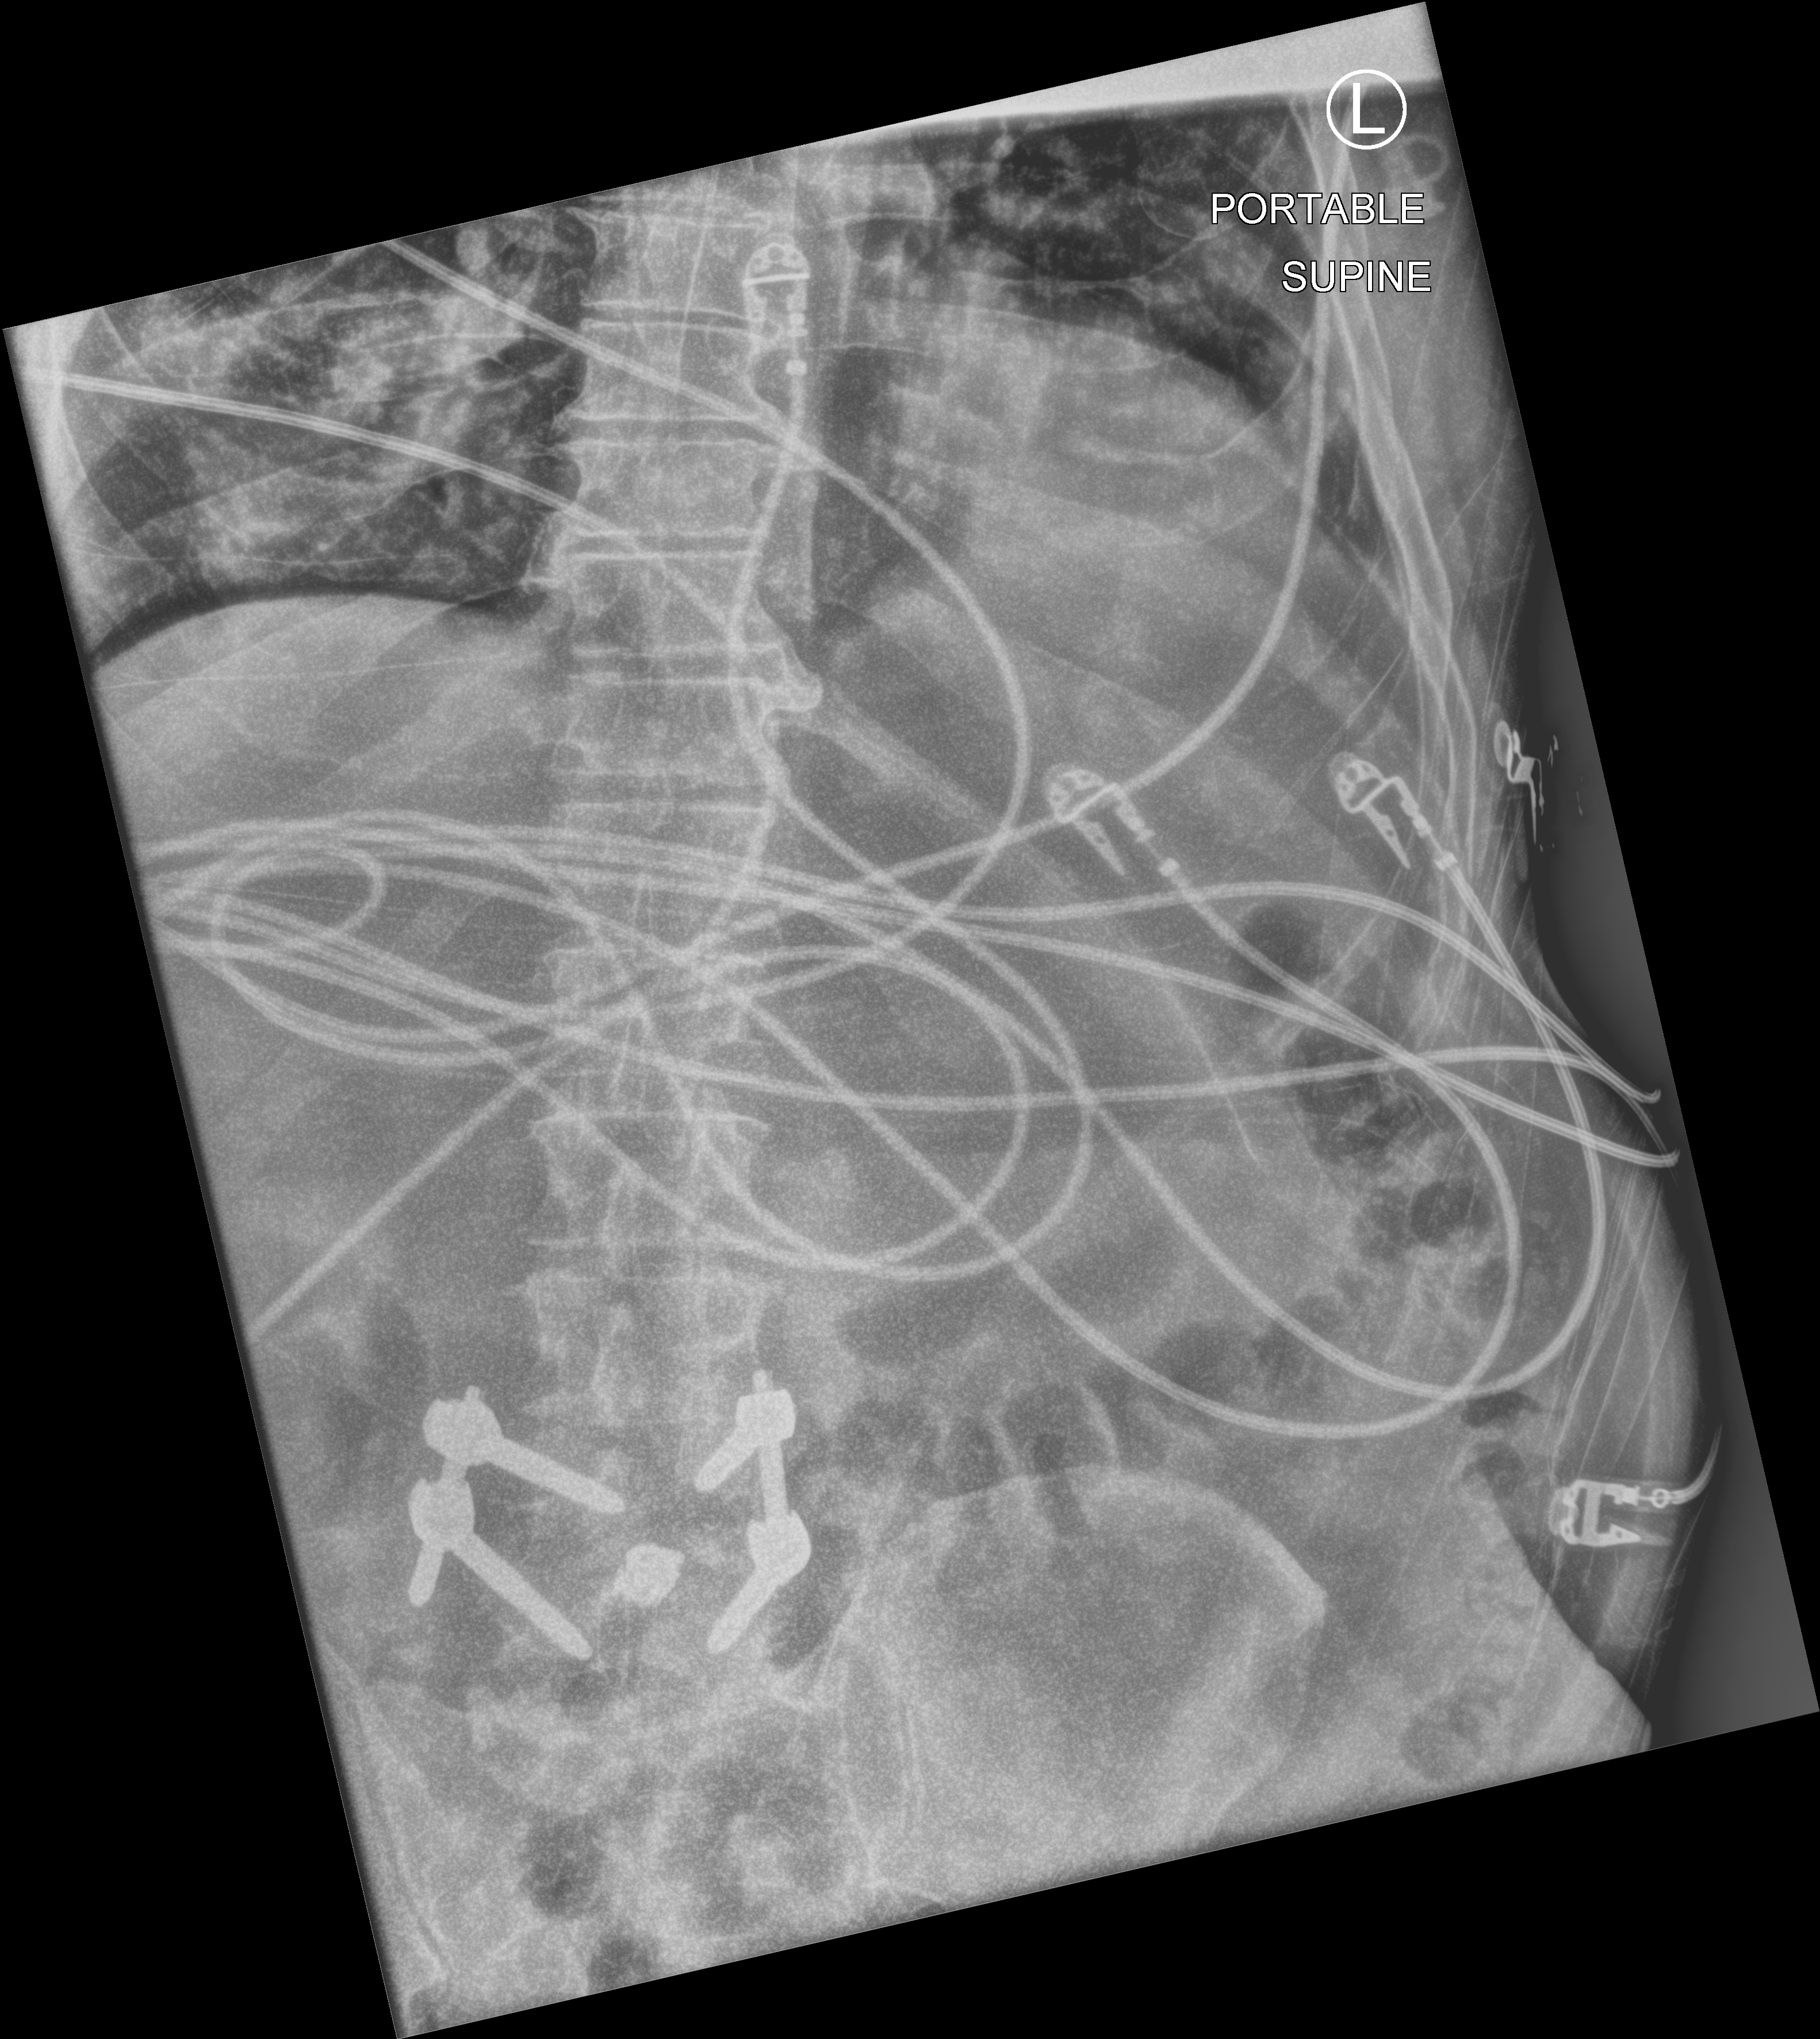
Portable abdomen radiograph. Male patient hospitalised with COVID-19, age 60–74 years.
Hospital-stay facts (about this admission, not read from this image; timing relative to this image not recorded):
- admitted to intensive care during this hospital stay: yes
- mechanically ventilated during this hospital stay: yes